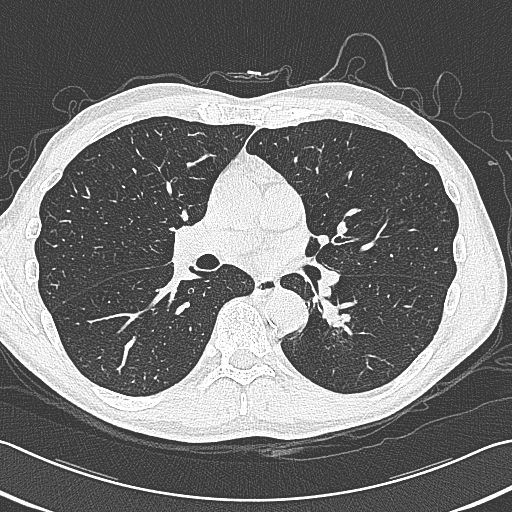
Chest CT (low-dose screening protocol), one axial image. First (baseline) screen. Lung window (W 1500 / L -600 HU). 120 kVp. Slice 162 of 354 in the series. Male participant, aged 59 years at enrolment. Former smoker at enrolment.
- Expert reader's lesion annotation, box from (x=314, y=292) to (x=375, y=352) px.
- Reader record for this screening exam (exam-level; its link to the box is not recorded): non-calcified nodule or mass ≥4 mm, left lower lobe, 15 × 15 mm, smooth margins, soft tissue attenuation.
- Lung cancer was diagnosed 17 days after this screen: squamous cell carcinoma, large cell, nonkeratinizing, NOS, left lower lobe, poorly differentiated (G3), stage IB (AJCC 6th edition), 31 mm at pathology.